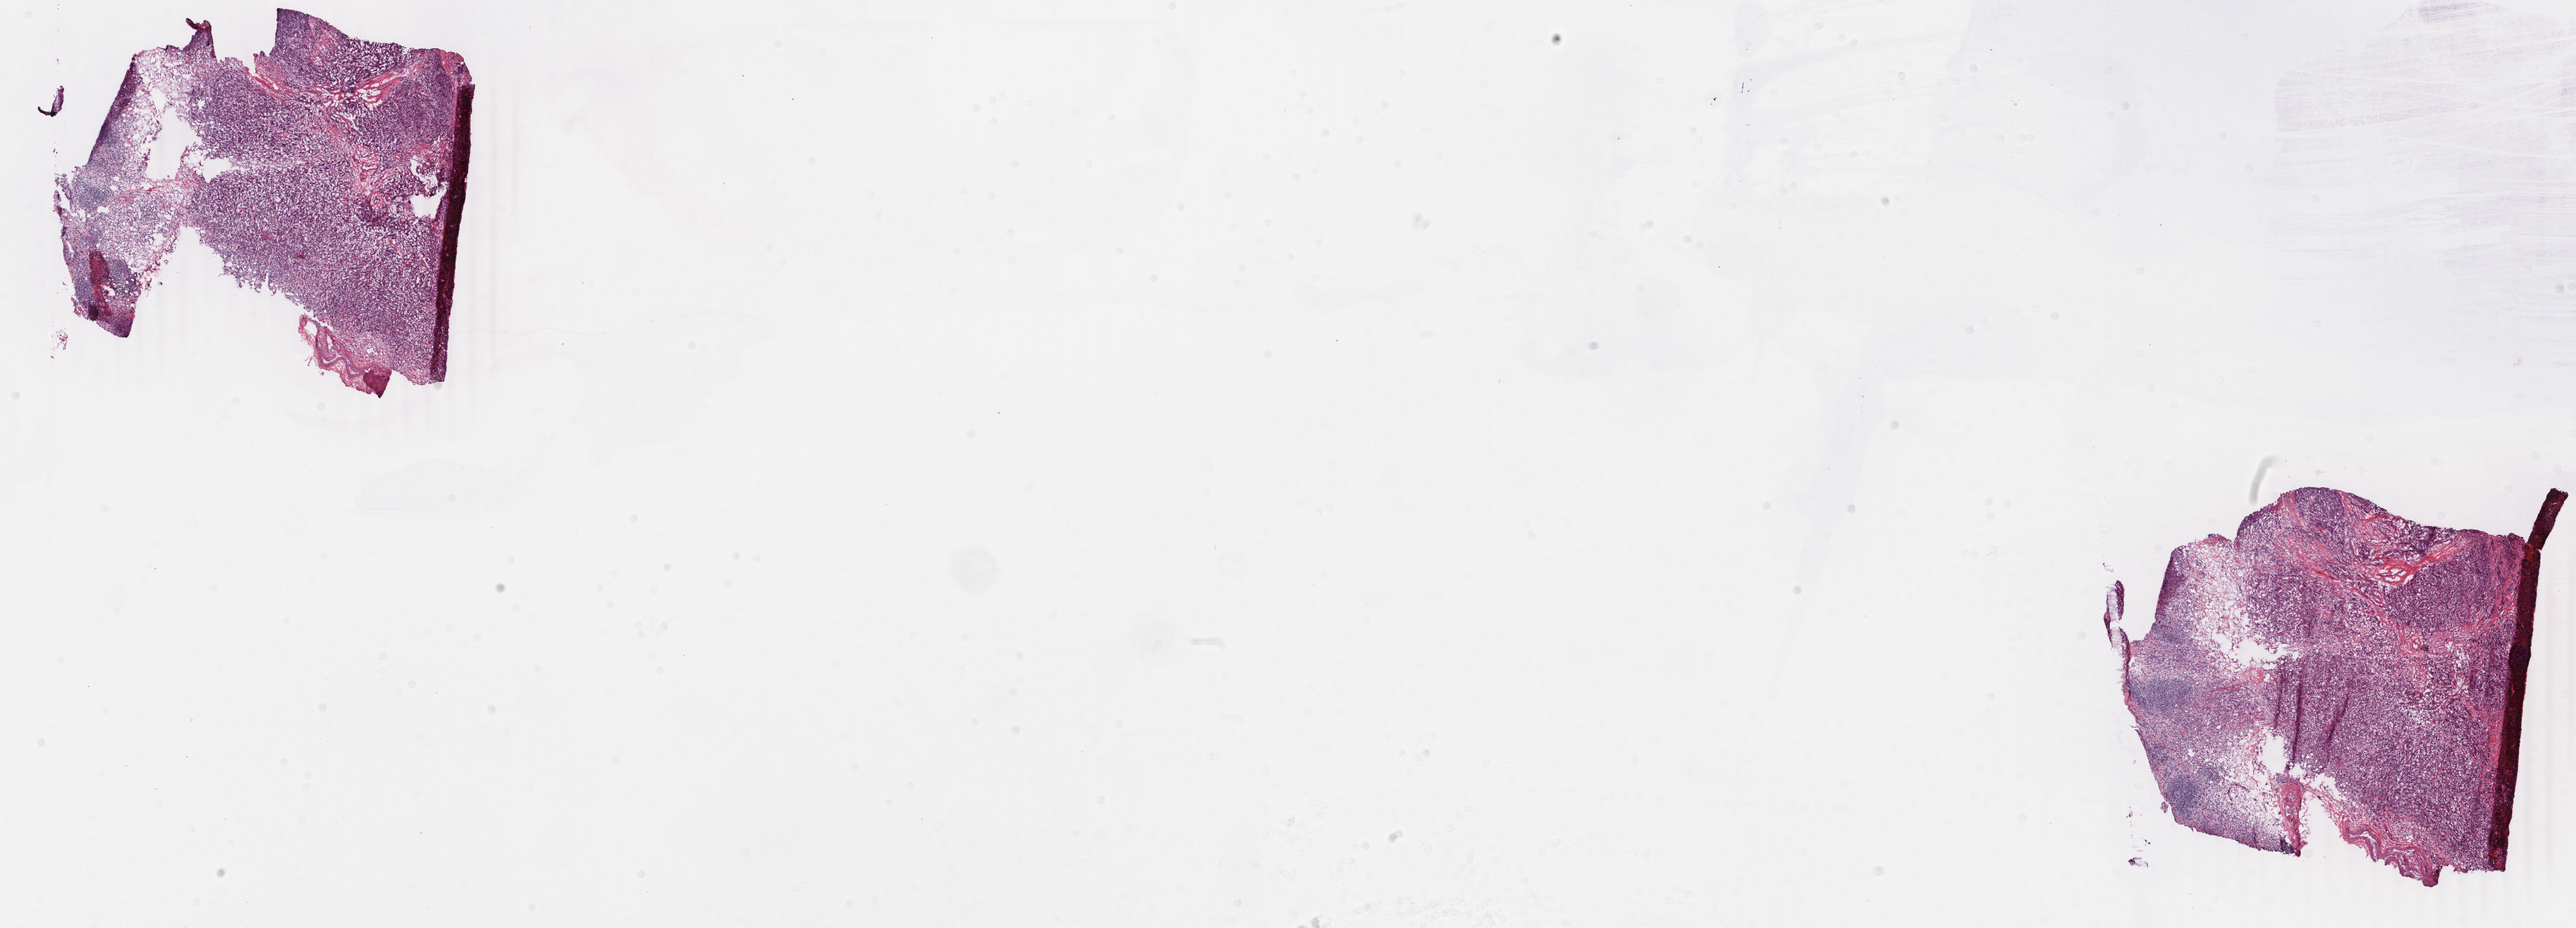
Whole-slide histology image, Hematoxylin and eosin (H&E) stained, low-resolution overview of the scanned area, about 27.6 x 9.9 mm; frozen section from the bottom of the tissue portion; primary tumour sample from the breast. Patient: female, age at initial diagnosis 66 years. Composition of this section per pathologist review: tumour cells 83%, tumour nuclei 90%, normal cells 1%, stromal cells 15%, necrosis 2%. Inflammatory infiltration, as recorded: lymphocyte infiltration 1%, monocyte infiltration 1%, neutrophil infiltration 0%.
• TNM: T2 N0 M0
• laterality: left
• AJCC pathologic stage: IIA
• diagnosis: Infiltrating duct carcinoma, NOS